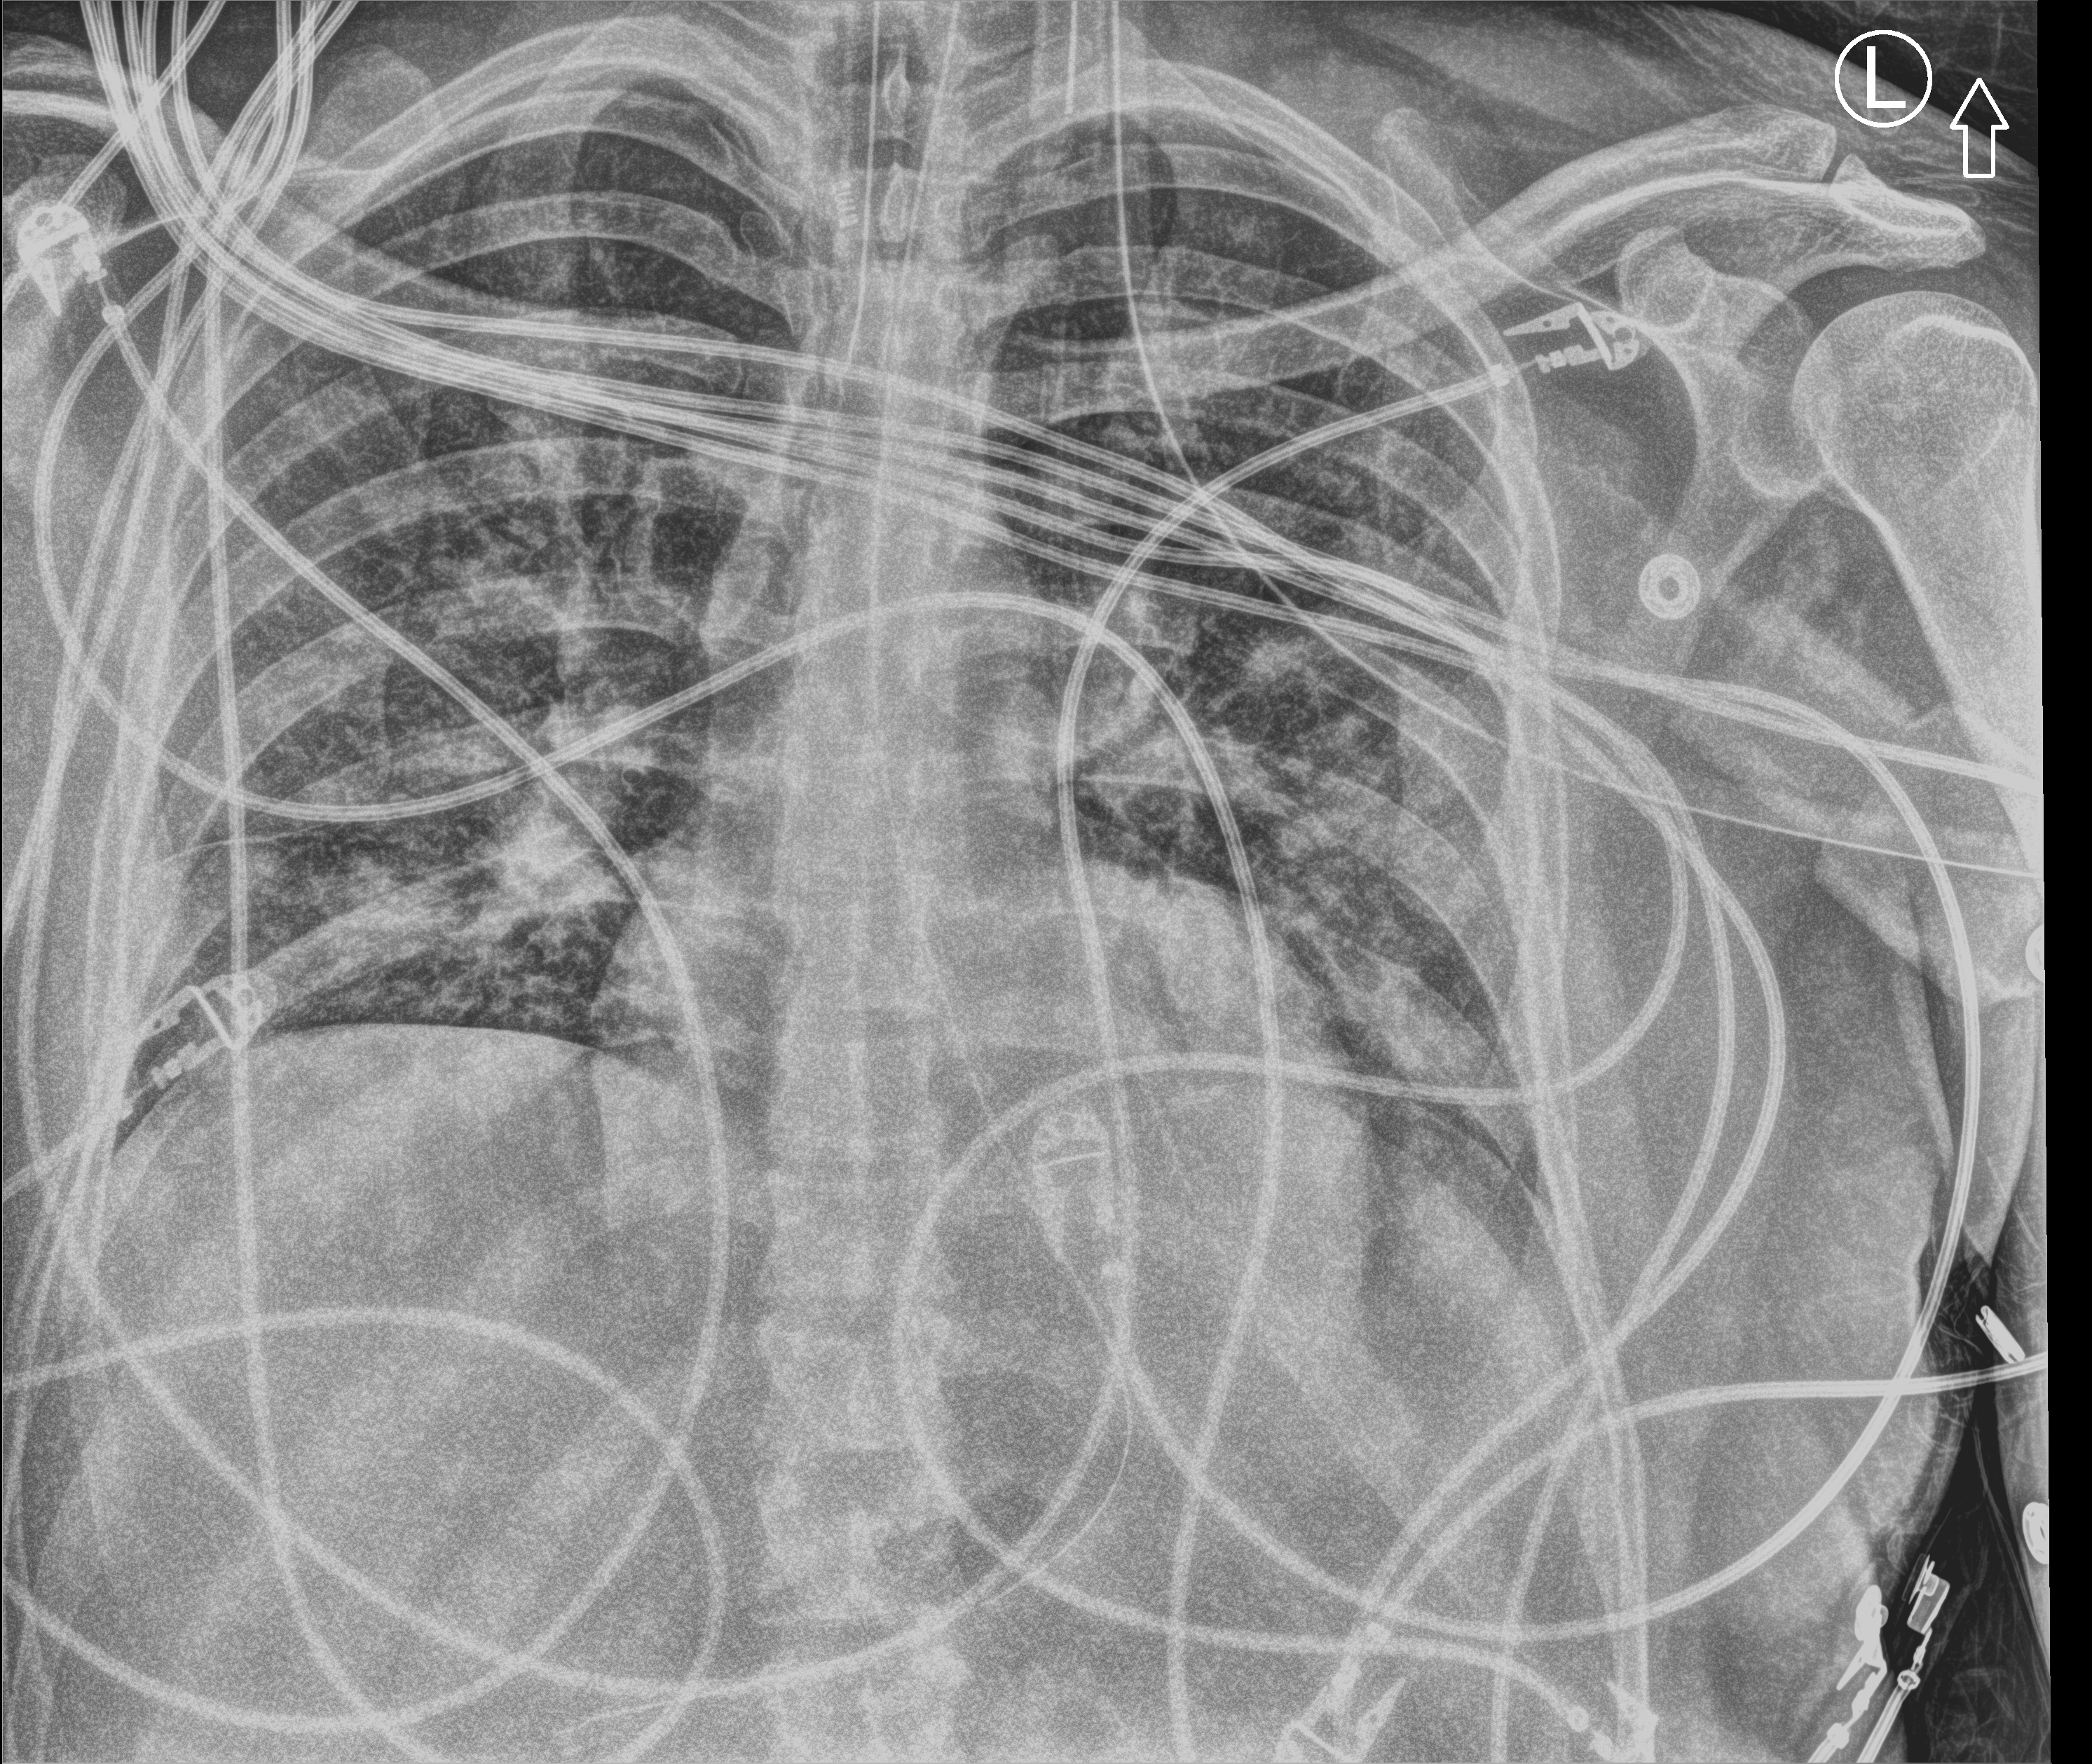
Bedside chest radiograph (computed radiography), anteroposterior (AP) projection. Male patient hospitalised with COVID-19, age 18–59 years.
From the hospital-stay record, not from the radiograph (when in the stay this image was taken is not recorded):
- mechanically ventilated during this hospital stay: yes
- diabetes (admission record): no
- admitted to intensive care during this hospital stay: yes